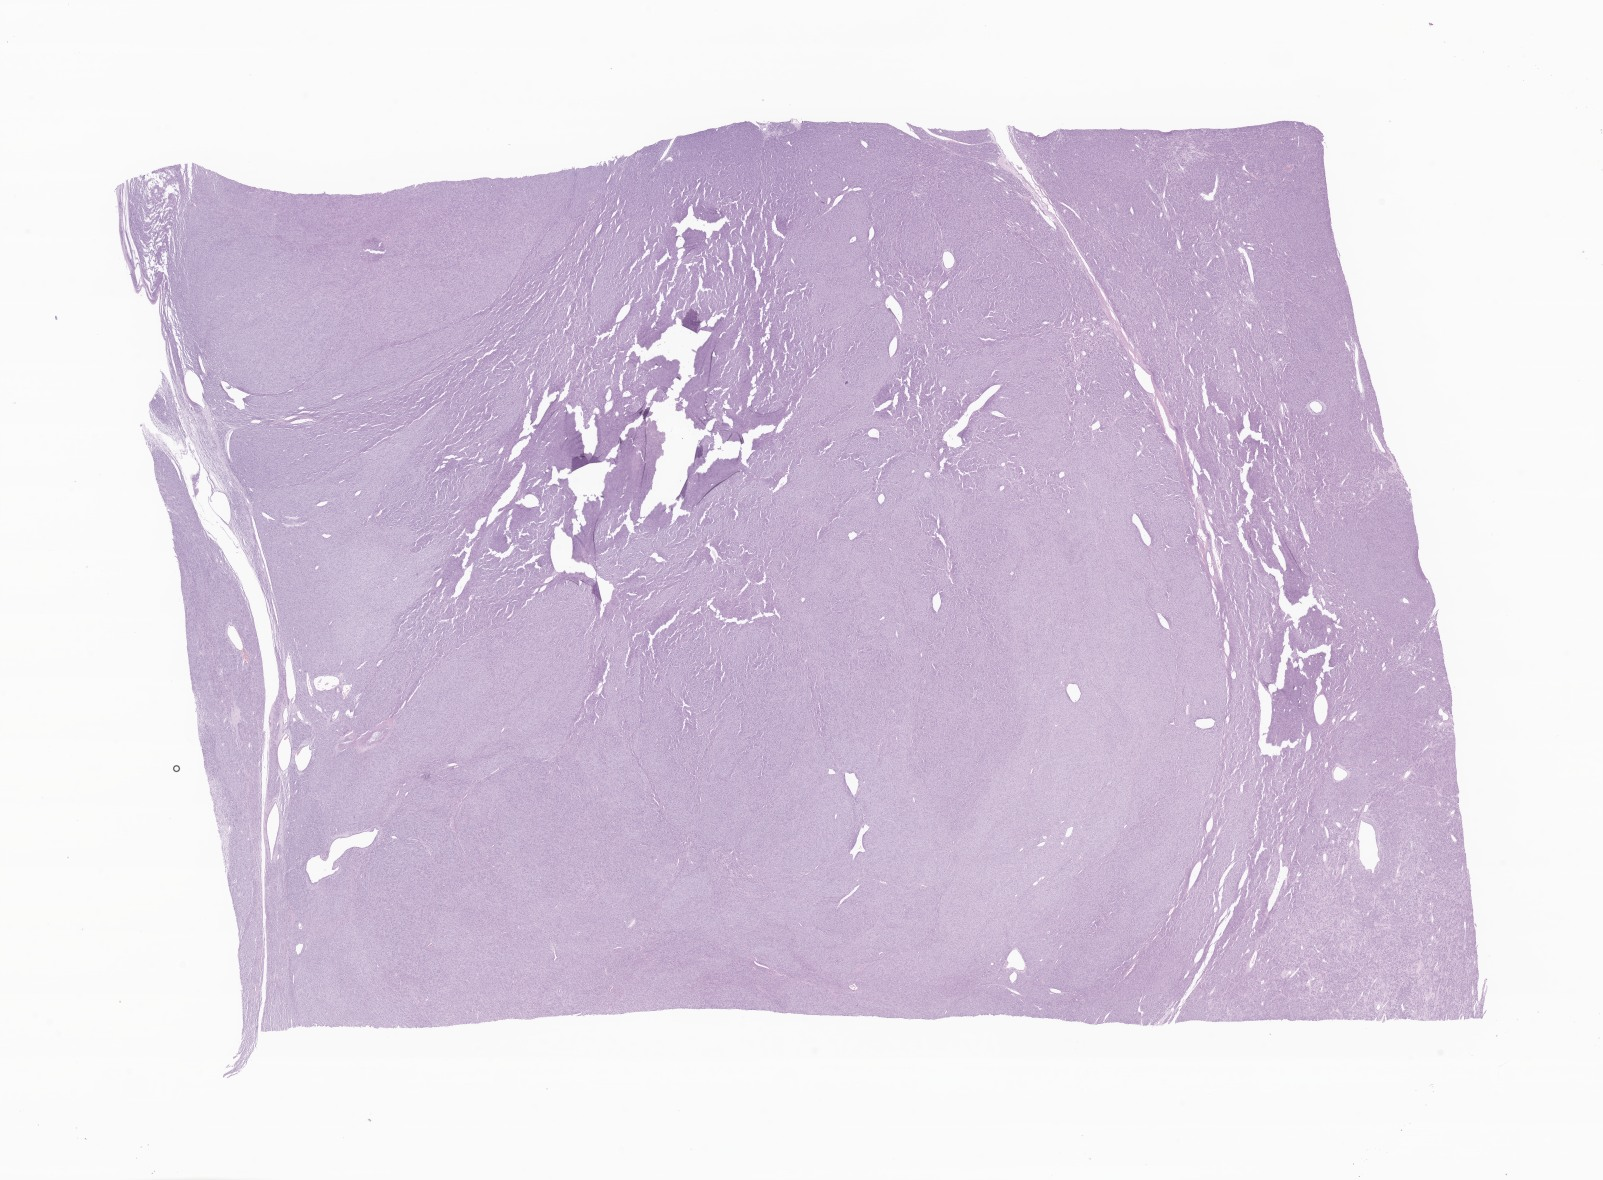
Whole-slide image, hematoxylin and eosin (H&E) stain of tumor tissue from the soft tissue of abdomen — whole scanned area (about 27.0 x 19.9 mm) shown as a low-resolution overview, FFPE section. Patient male; age 223 months (18 years 7 months).
Diagnosis: Gastrointestinal stromal tumor, NOS.